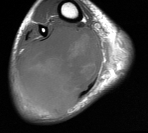
MRI of an extremity soft-tissue mass, one axial slice; MR volume resampled by the dataset authors to the PET/CT grid (not the native acquisition matrix); 148 × 133 image matrix. Male patient. From the clinical record (not read from this slice): histological type: liposarcoma - round cell; grade: high; site of the primary tumour: right calf.
Structures marked on this image (expert contour drawn on MRI and transferred to this co-registered scan by the dataset authors):
- gross tumour volume (mass): bounding box (x1, y1, x2, y2) in pixels: (15, 25, 103, 113)